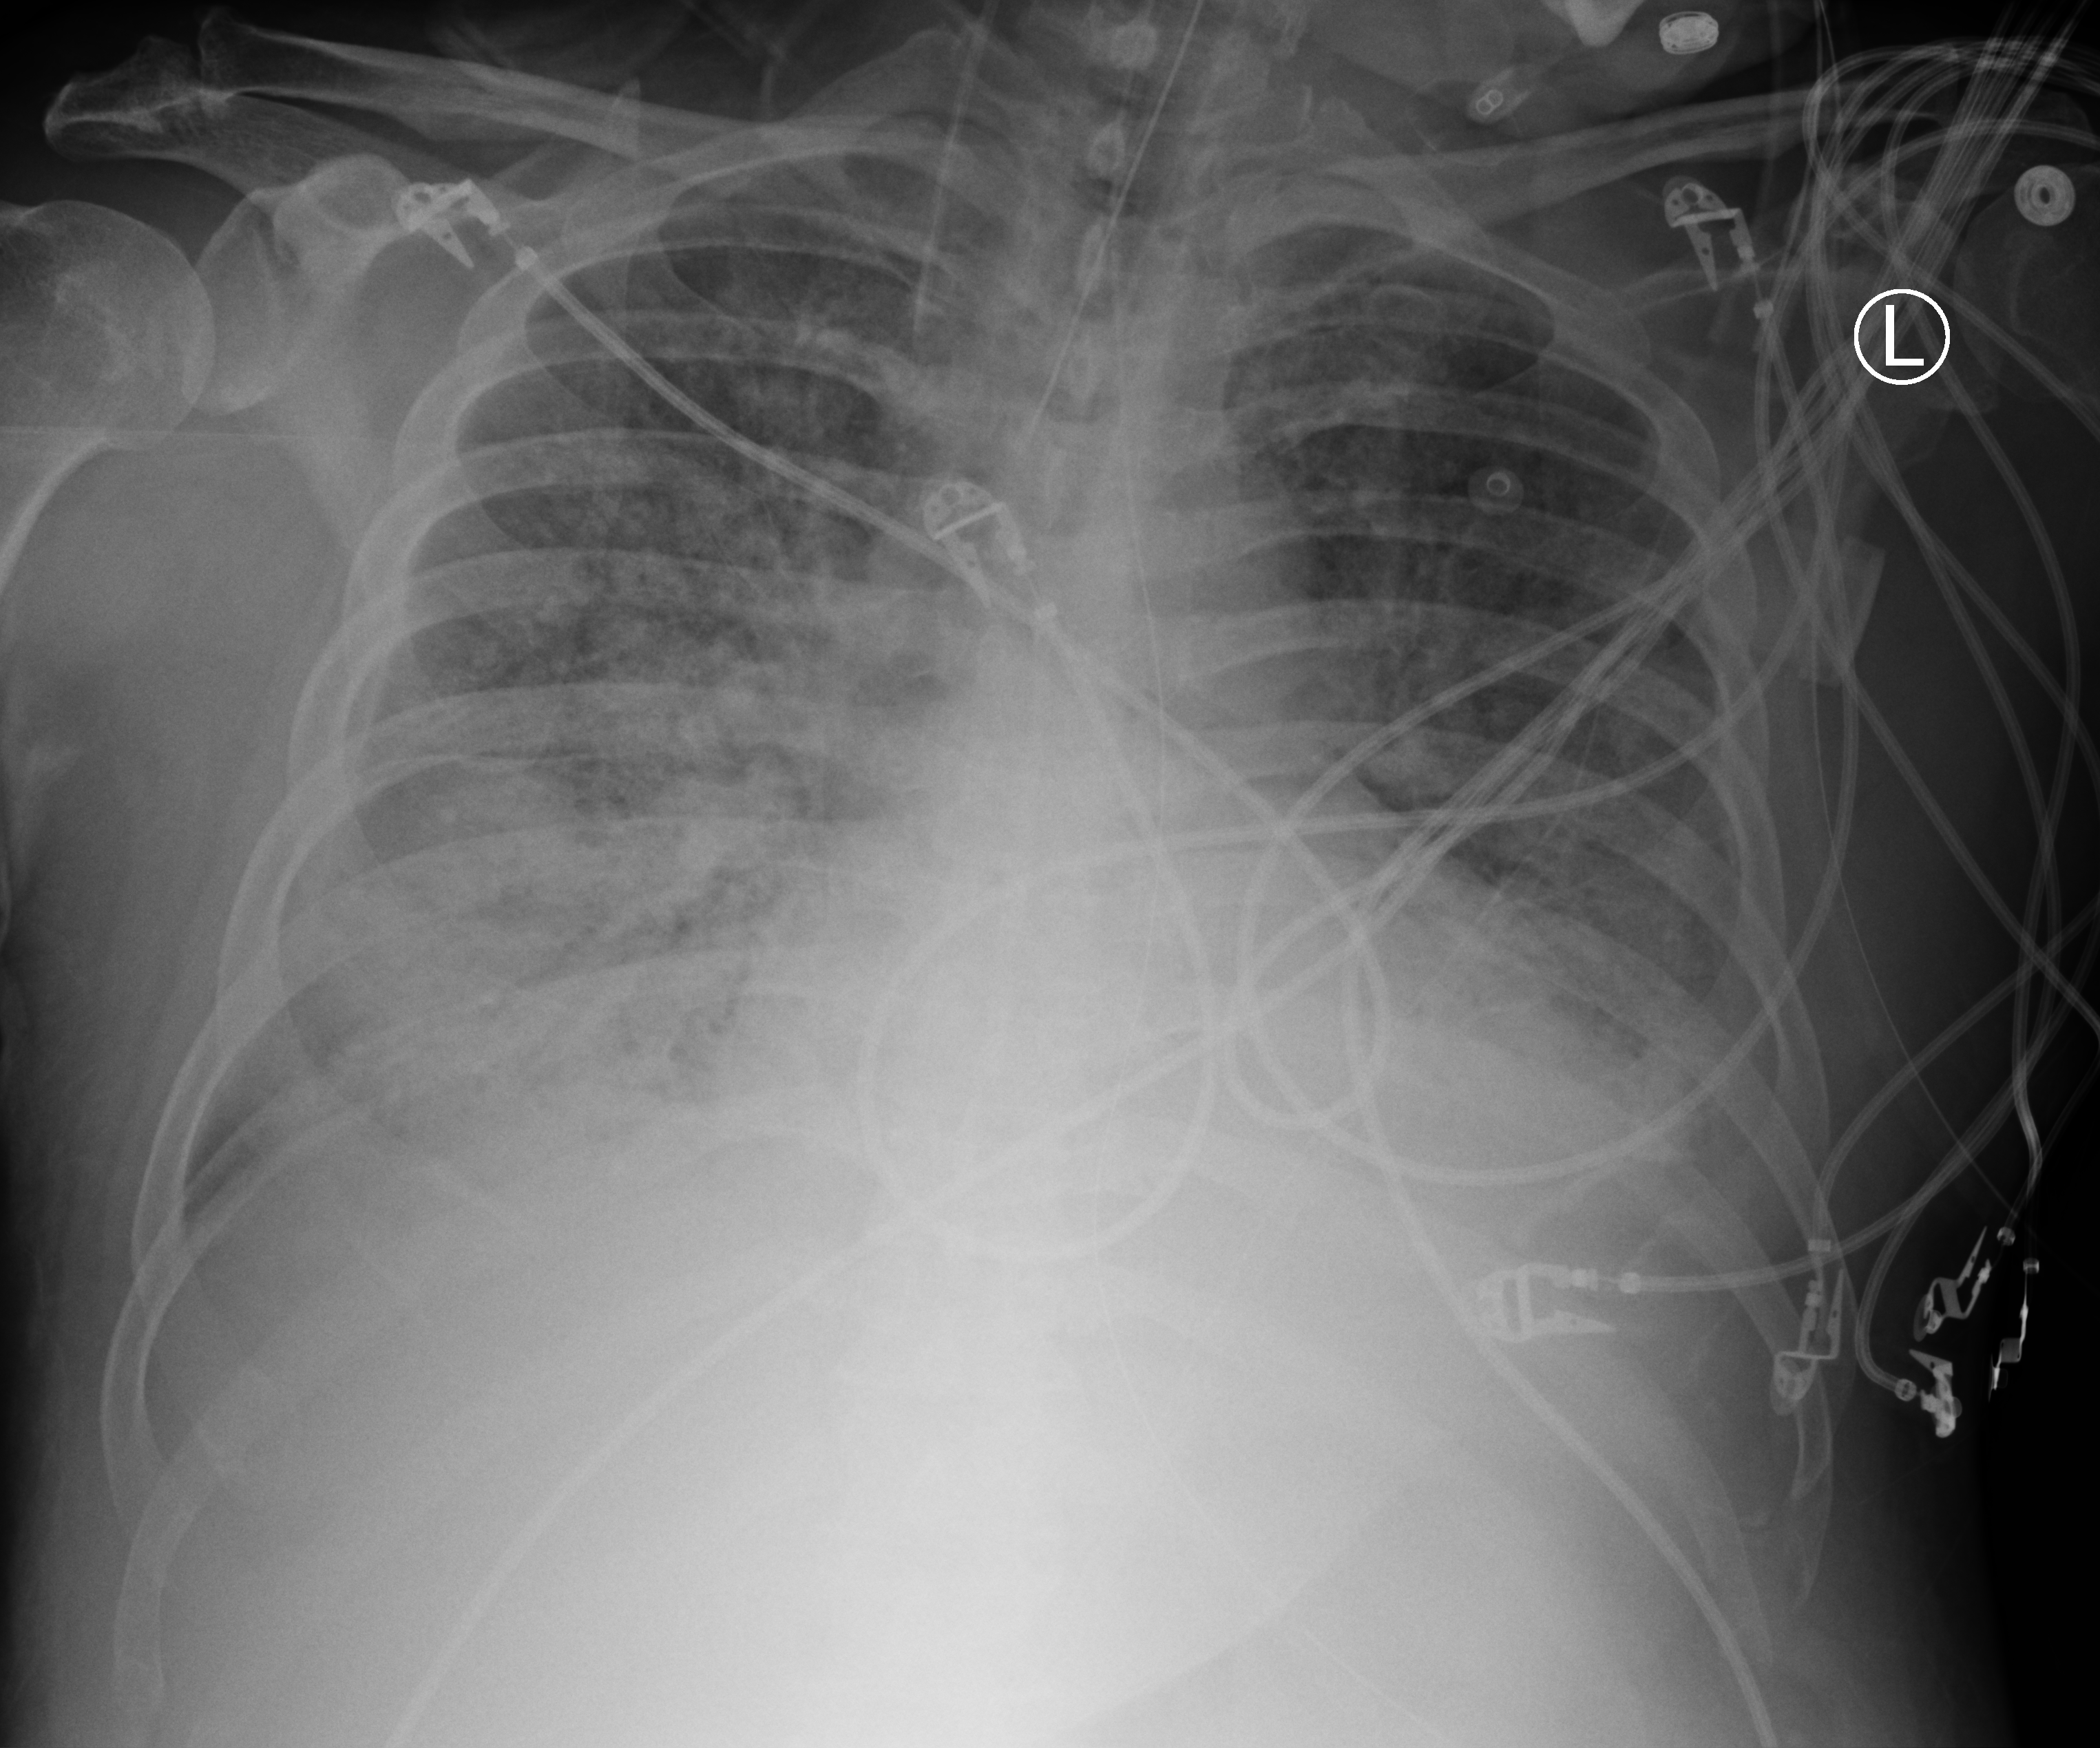
Portable chest radiograph; anteroposterior (AP) projection. Patient hospitalised with COVID-19; male, aged 60–74 years.
Admission-level facts for this patient (not findings on this image; timing relative to this image not recorded): COPD (admission record): no.